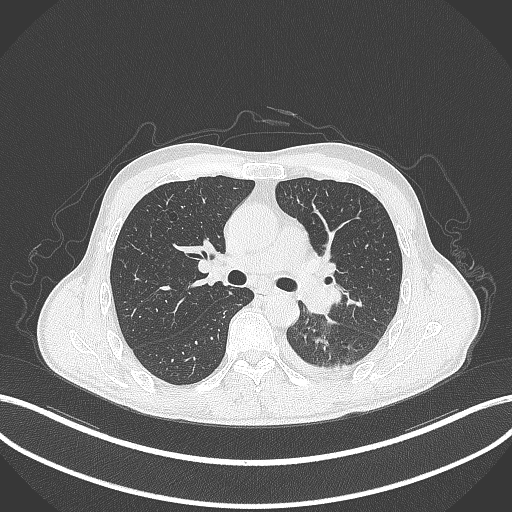
Chest CT, one axial slice; position 199 of 295 along the scan axis; 120 kVp; lung window (W 1500 / L -600 HU); 1 mm slice thickness; 512 × 512 image matrix. Patient: male, 47 years. From the clinical record (not read from this slice): clinical TNM (as recorded): T3 N1 M1c; histopathological grade: G3.
Structures marked on this image (rectangle marked by the reading radiologist):
- lung tumour (recorded histology: small cell carcinoma): box from (x=295, y=274) to (x=345, y=316) px